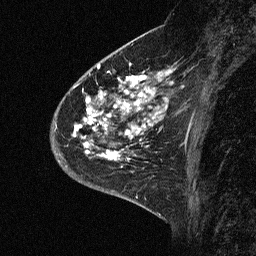
Breast MRI (dynamic contrast-enhanced), one sagittal slice. Slice 21 of 64 in the series (ordered by position). Dynamic contrast-enhanced study with each time point stored as its own series, time point 2 of 3 at this slice position (early post-contrast, ordered by acquisition time). 1.5 T. TE 4.5 ms, TR 11 ms. 256 × 256 image matrix, field of view 200 × 200 mm. Patient: female, 46 years. From the clinical record (not read from this slice): setting: breast cancer imaged before/during neoadjuvant chemotherapy; receptor status: HER2-positive.
Annotated regions visible in this slice (semi-automatic segmentation, software-assisted and operator-edited):
- analysis volume of interest (the breast-tissue region the enhancement analysis was run in; not a lesion): bounding box <43,72,176,177> (left, top, right, bottom; pixels)
- tumour enhancement mask (voxels above the 90 % enhancement threshold inside the analysis volume of interest): <71,72,172,162>